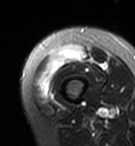
MRI of an extremity soft-tissue mass, one axial slice. Position 11 of 95 along the scan axis. T2-weighted fat-saturated. MR volume resampled by the dataset authors to the PET/CT grid (not the native acquisition matrix). 3.27 mm slice thickness. 135 × 146 image matrix, field of view 132 × 143 mm. Female patient. From the clinical record (not read from this slice): histological type: pleiomorphic undifferentiated sarcoma; grade: high; site of the primary tumour: right quadricep.
Annotated regions visible in this slice (expert contour drawn on MRI and transferred to this co-registered scan by the dataset authors):
- gross tumour volume including surrounding oedema: bounding box <35,45,86,96> (left, top, right, bottom; pixels)